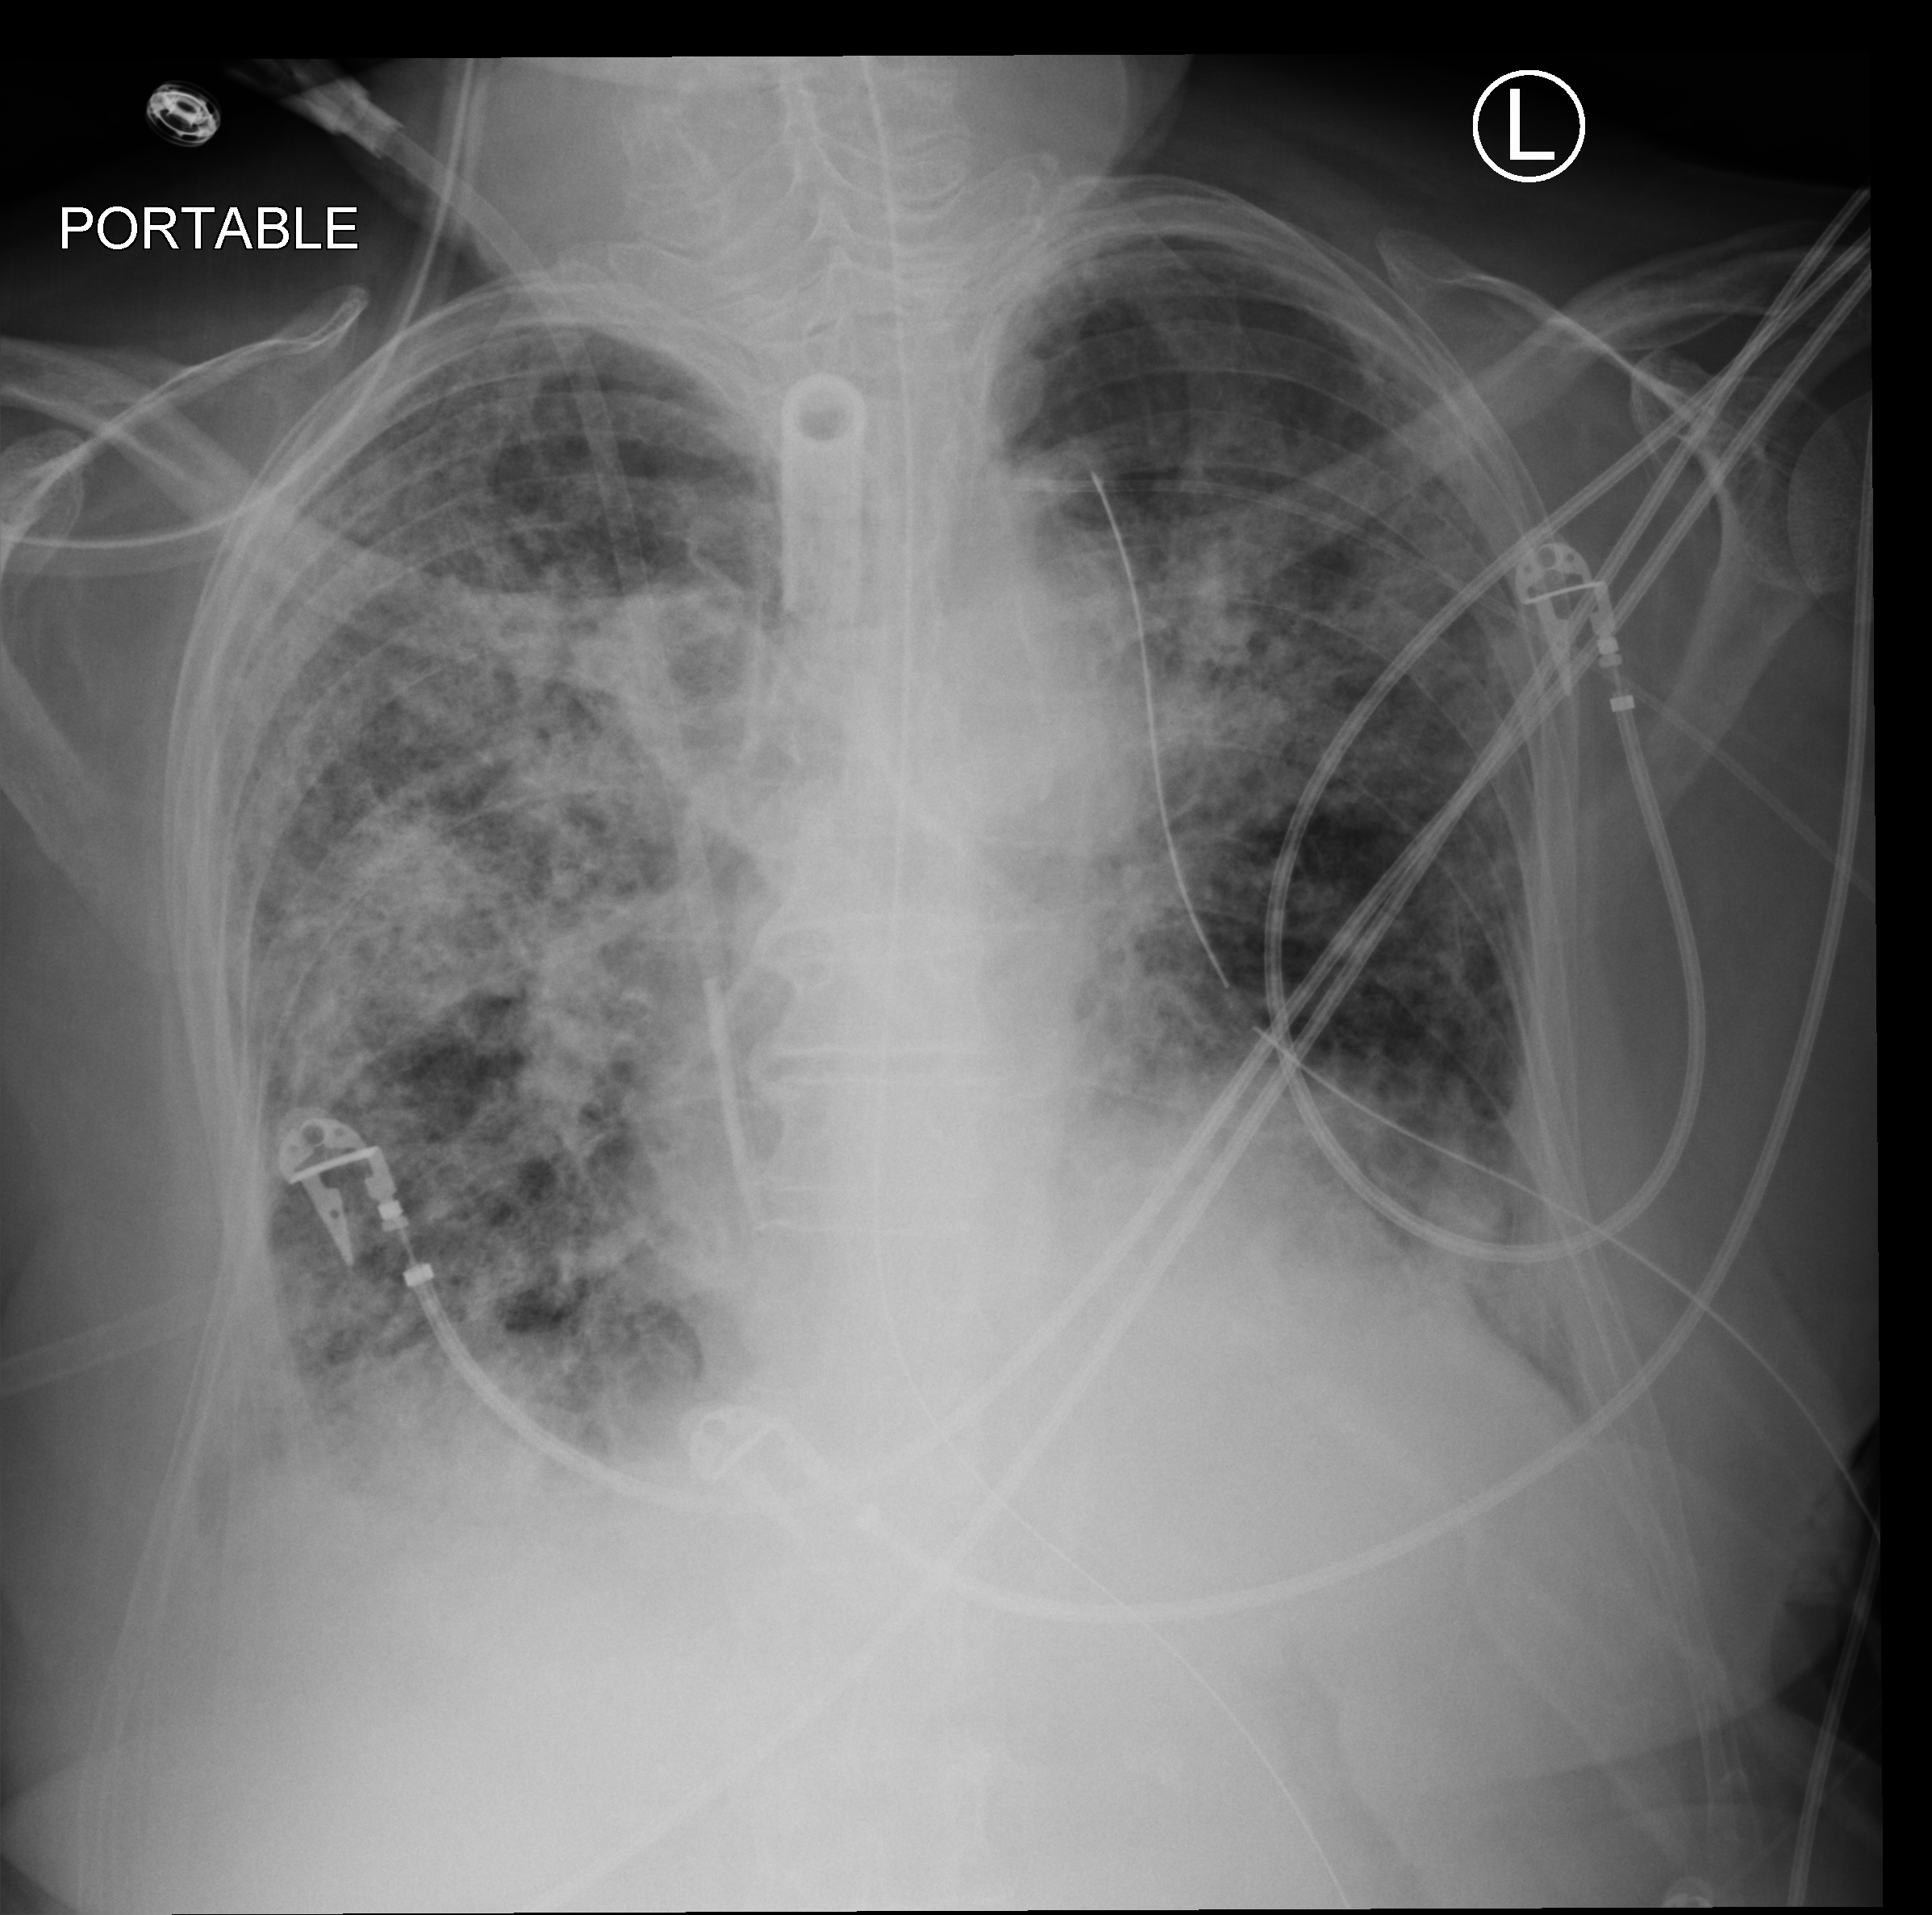
Chest X-ray (portable); anteroposterior (AP) projection. Female patient hospitalised with COVID-19, age 75–90 years.
From the hospital-stay record, not from the radiograph (when in the stay this image was taken is not recorded):
- length of hospital stay: 70 days
- hypertension (admission record): yes
- mechanically ventilated during this hospital stay: yes